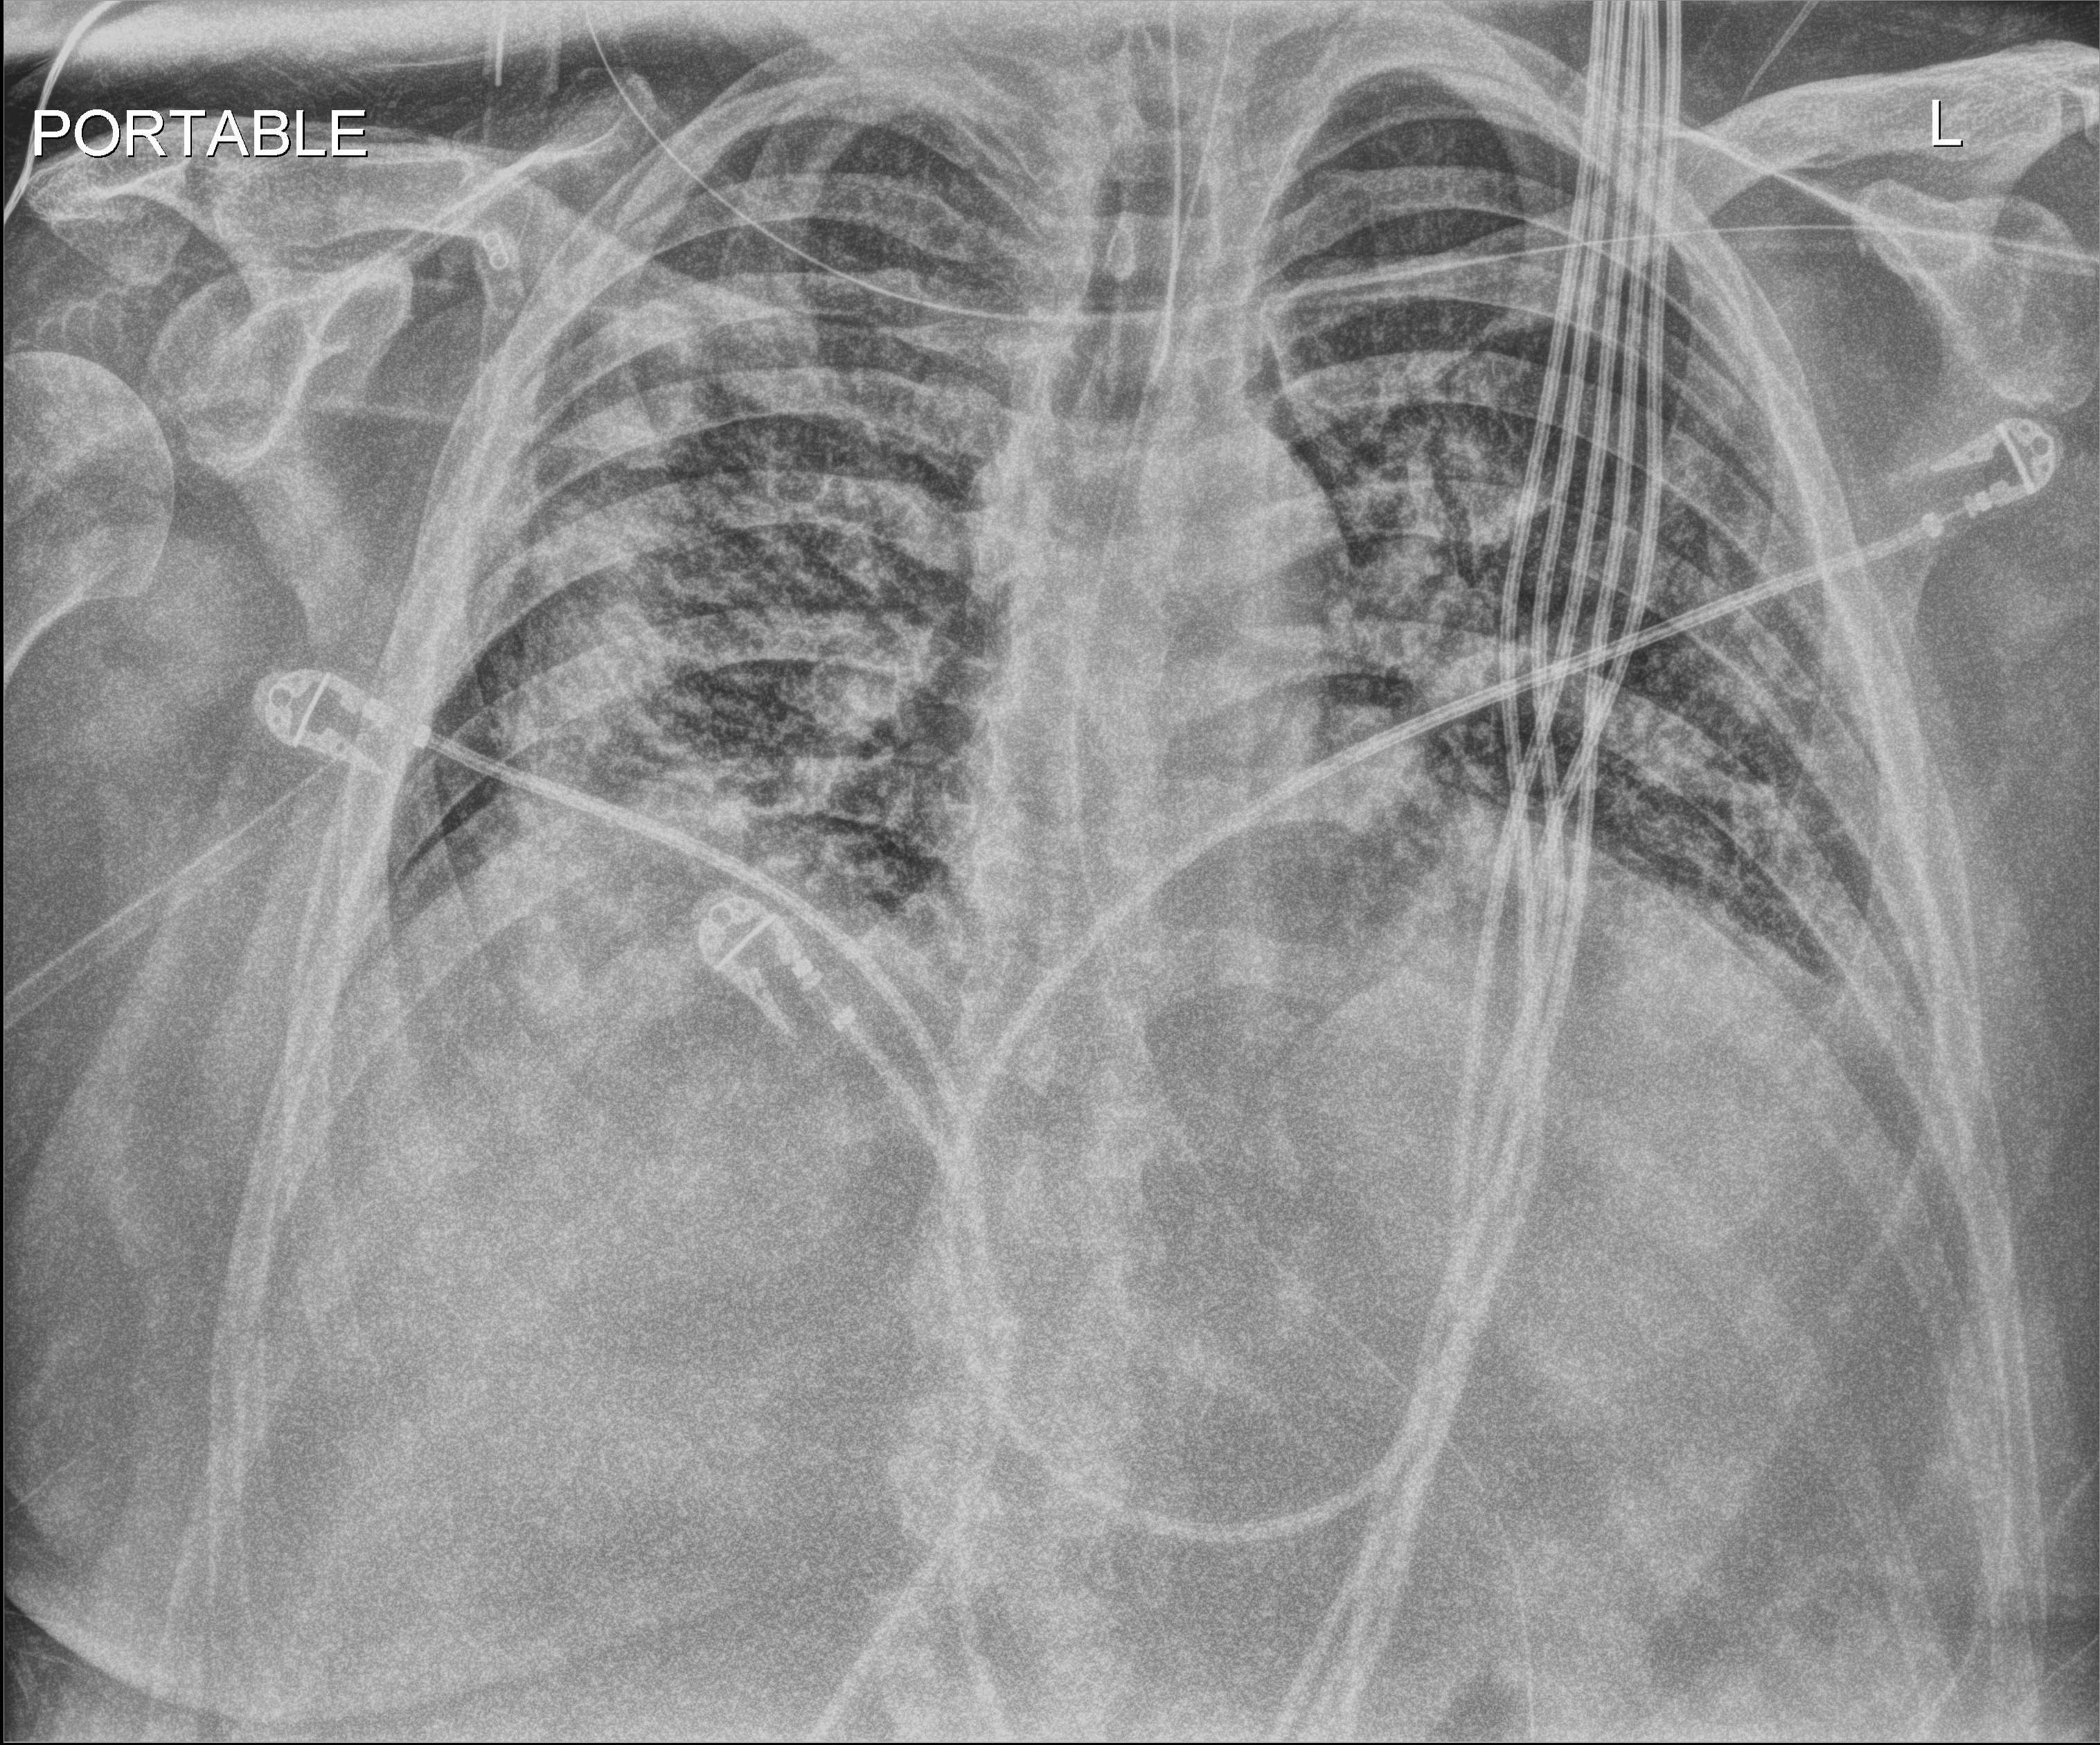
Portable chest radiograph; anteroposterior (AP) projection. Male patient hospitalised with COVID-19, age 18–59 years.
Hospital-stay facts (about this admission, not read from this image; timing relative to this image not recorded): mechanically ventilated during this hospital stay: yes; COPD (admission record): no; hypertension (admission record): yes.